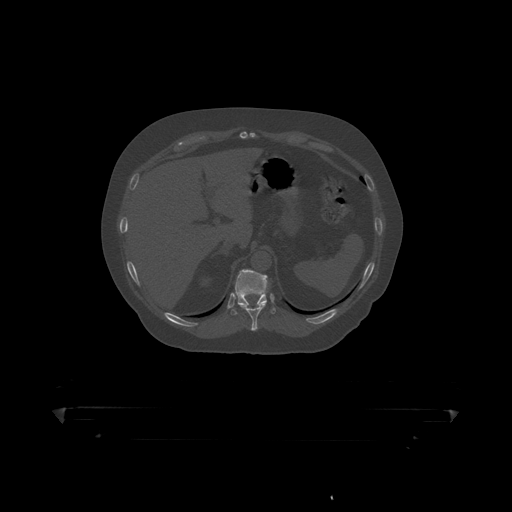
CT including the spine, one axial slice. Slice 205 of 390 in the series (ordered by position). Reconstruction kernel STANDARD. Bone window (W 1800 / L 400 HU). 512 × 512 image matrix, field of view 650 × 650 mm. Male patient, age 60 years. From the clinical record (not read from this slice): primary cancer: prostate.
Annotated regions visible in this slice (semi-automatically segmented with operator editing):
- T10 vertebra: bounding box (x1, y1, x2, y2) in pixels: (240, 302, 267, 319)
- T11 vertebra: (231, 270, 276, 316)